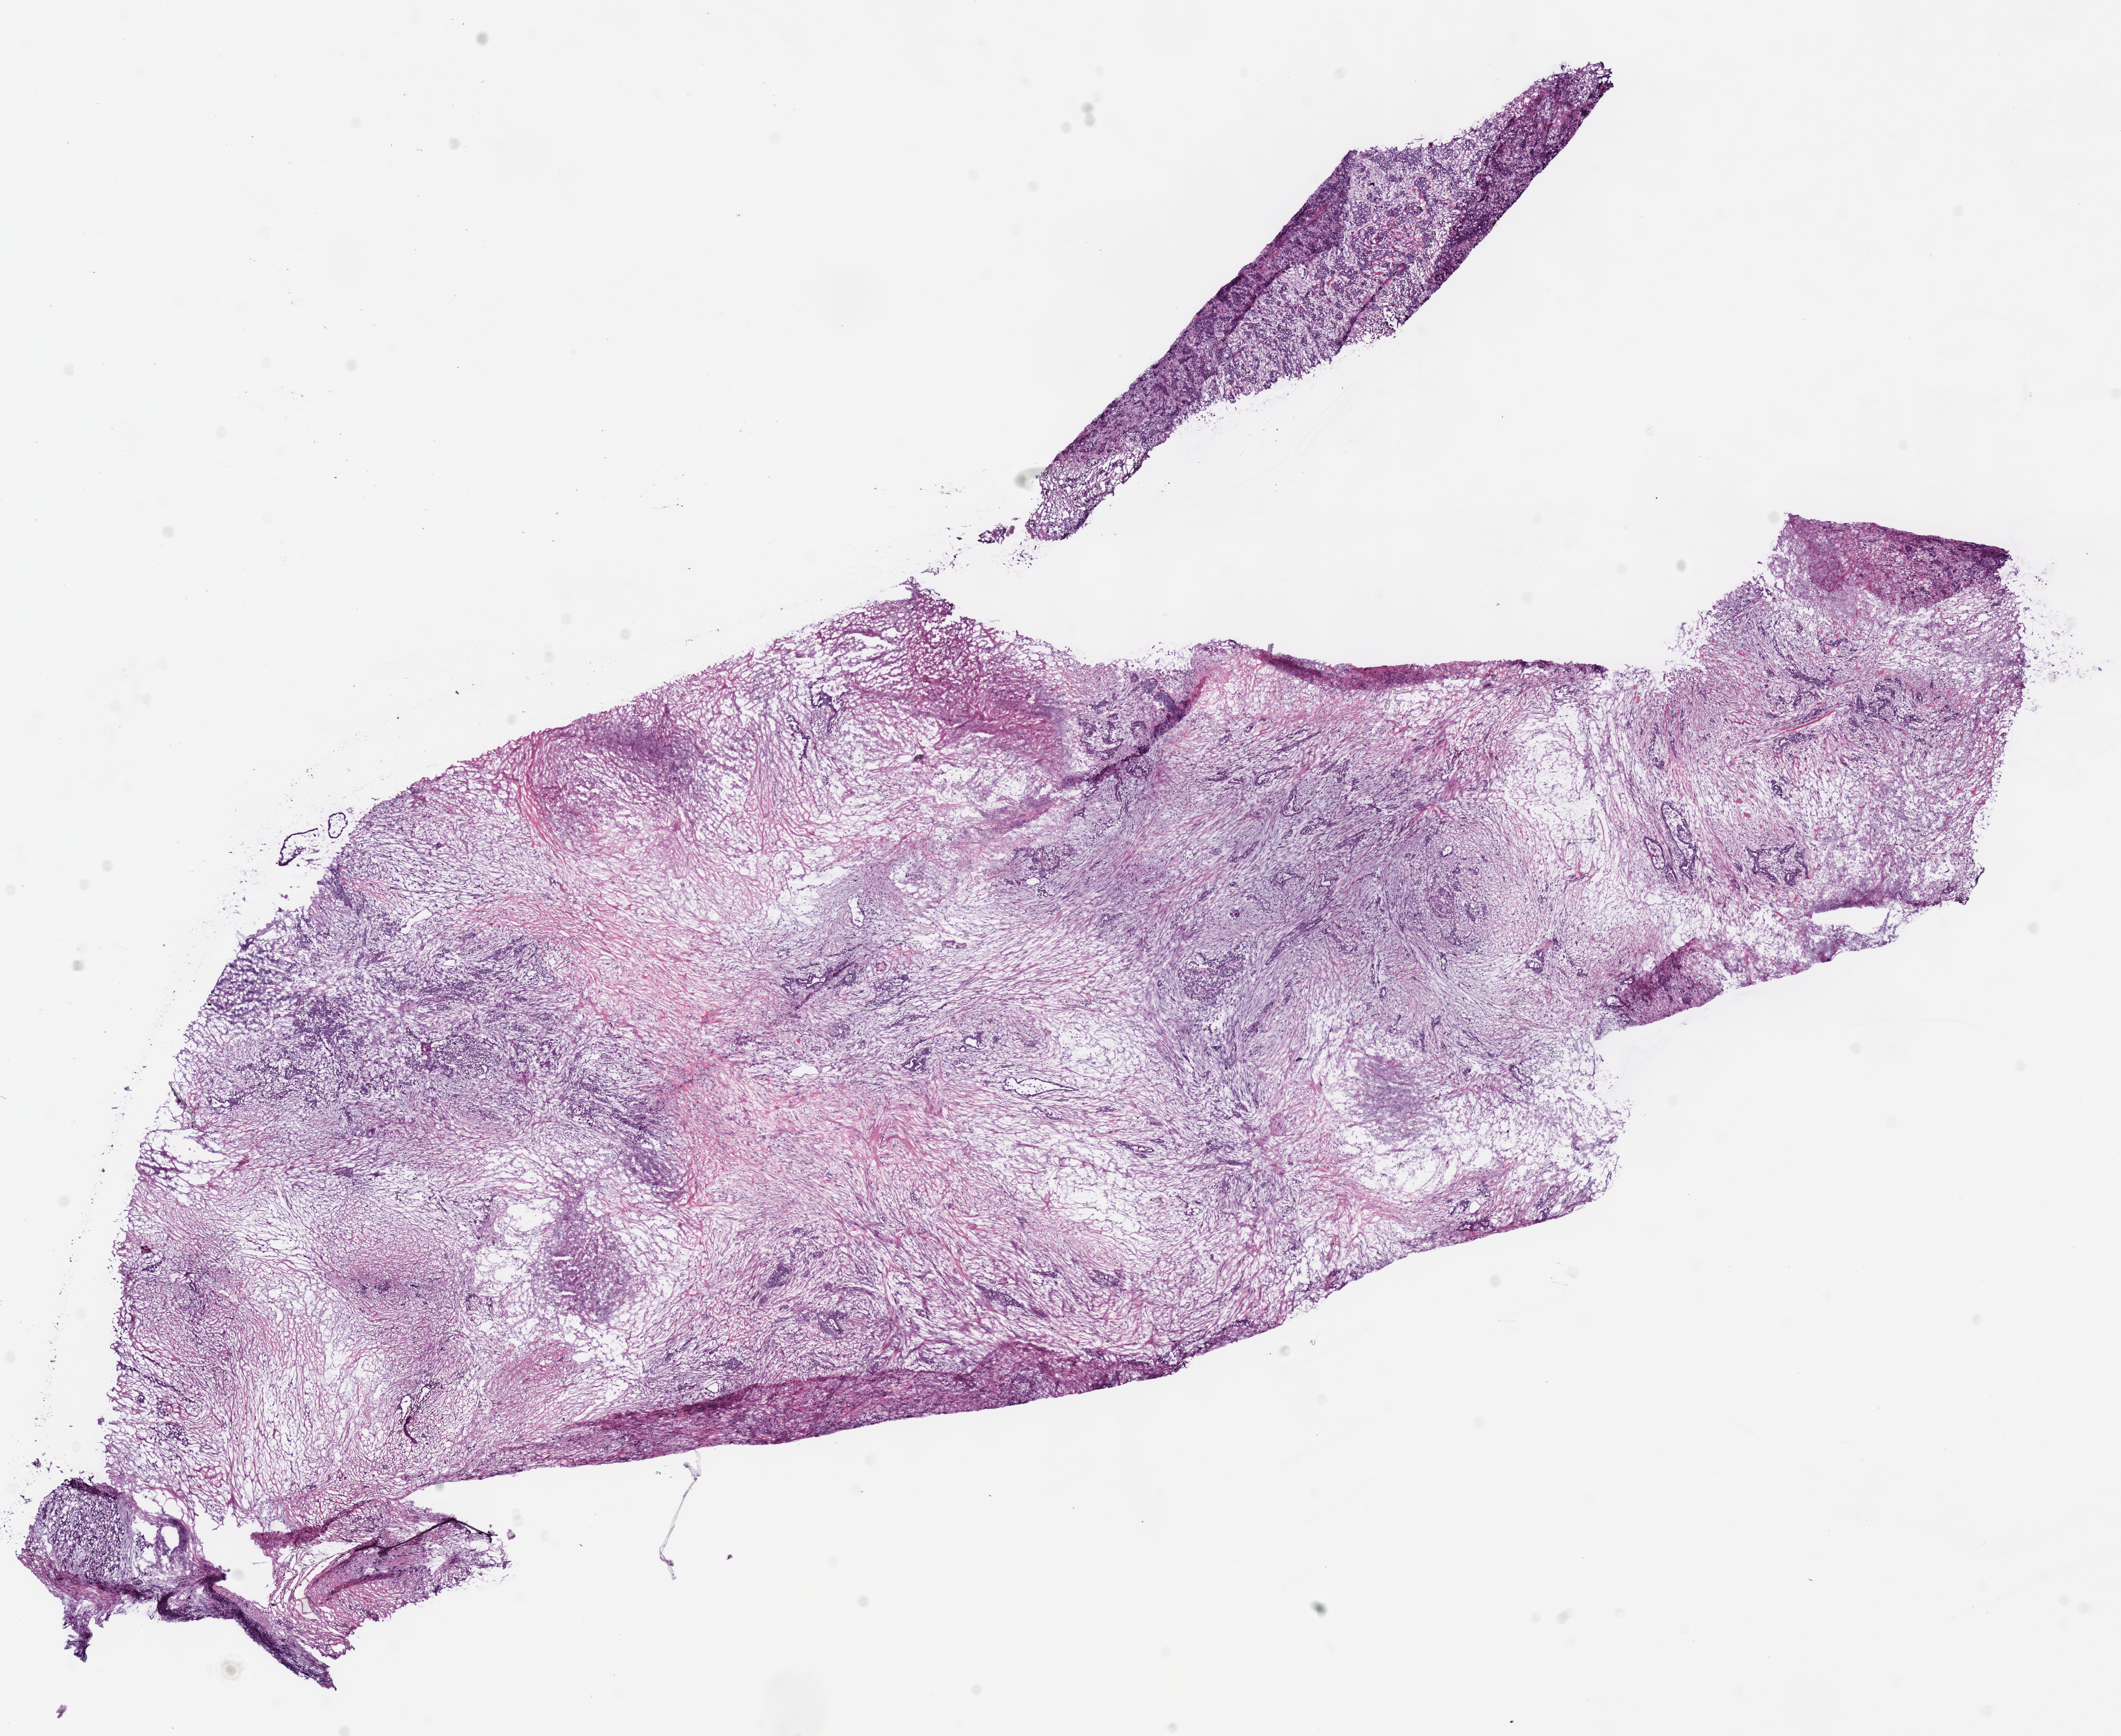
Whole-slide histology image, Hematoxylin and eosin (H&E) stained — a low-resolution overview of the entire scanned area, about 14.2 x 11.6 mm (slide scanned at 40x), frozen section from the top of the tissue portion, sample: primary tumour, pancreas. Male, age 81 years at initial diagnosis. Slide review estimates, as recorded: tumour cells 25%, tumour nuclei 30%.
Diagnosis: Infiltrating duct carcinoma, NOS.